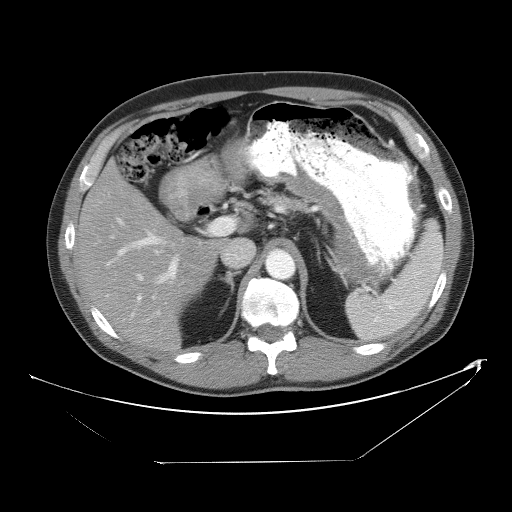
Contrast-enhanced abdominal CT, one axial slice. Slice 33 of 53 in the series (ordered by position). 120 kVp. Intravenous contrast given. Soft-tissue window (W 400 / L 40 HU). 5 mm slice thickness. 512 × 512 image matrix, field of view 438 × 438 mm. Male patient, age 59 years. Case-level facts recorded for this patient, not image findings: diagnosis: colorectal cancer liver metastases, imaged before liver resection; multiple liver metastases: yes; largest metastasis: 8.5 cm; chemotherapy before resection: yes.
Annotated regions visible in this slice (manually delineated by an expert):
- hepatic veins: bounding box [x1, y1, x2, y2] px = [110, 217, 163, 300]
- liver: [77, 165, 220, 354]
- planned liver remnant (the part of the liver to remain after resection): [77, 165, 221, 353]
- portal vein (with intrahepatic branches): [109, 219, 233, 299]